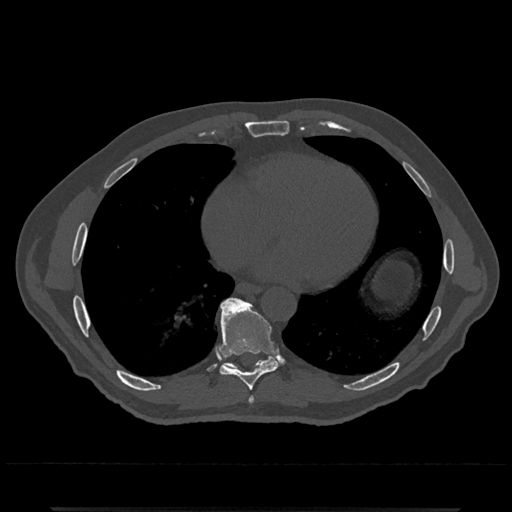
CT including the spine, one axial slice. 120 kVp. Bone window (W 1800 / L 400 HU). 512 × 512 image matrix. Male patient, age 67 years. Case-level facts recorded for this patient, not image findings: primary cancer: prostate.
Structures marked on this image (semi-automatic segmentation, software-assisted and operator-edited):
- T7 vertebra: bounding box <249,396,254,403> (left, top, right, bottom; pixels)
- T8 vertebra: <219,297,282,391>
- T9 vertebra: <219,298,278,370>